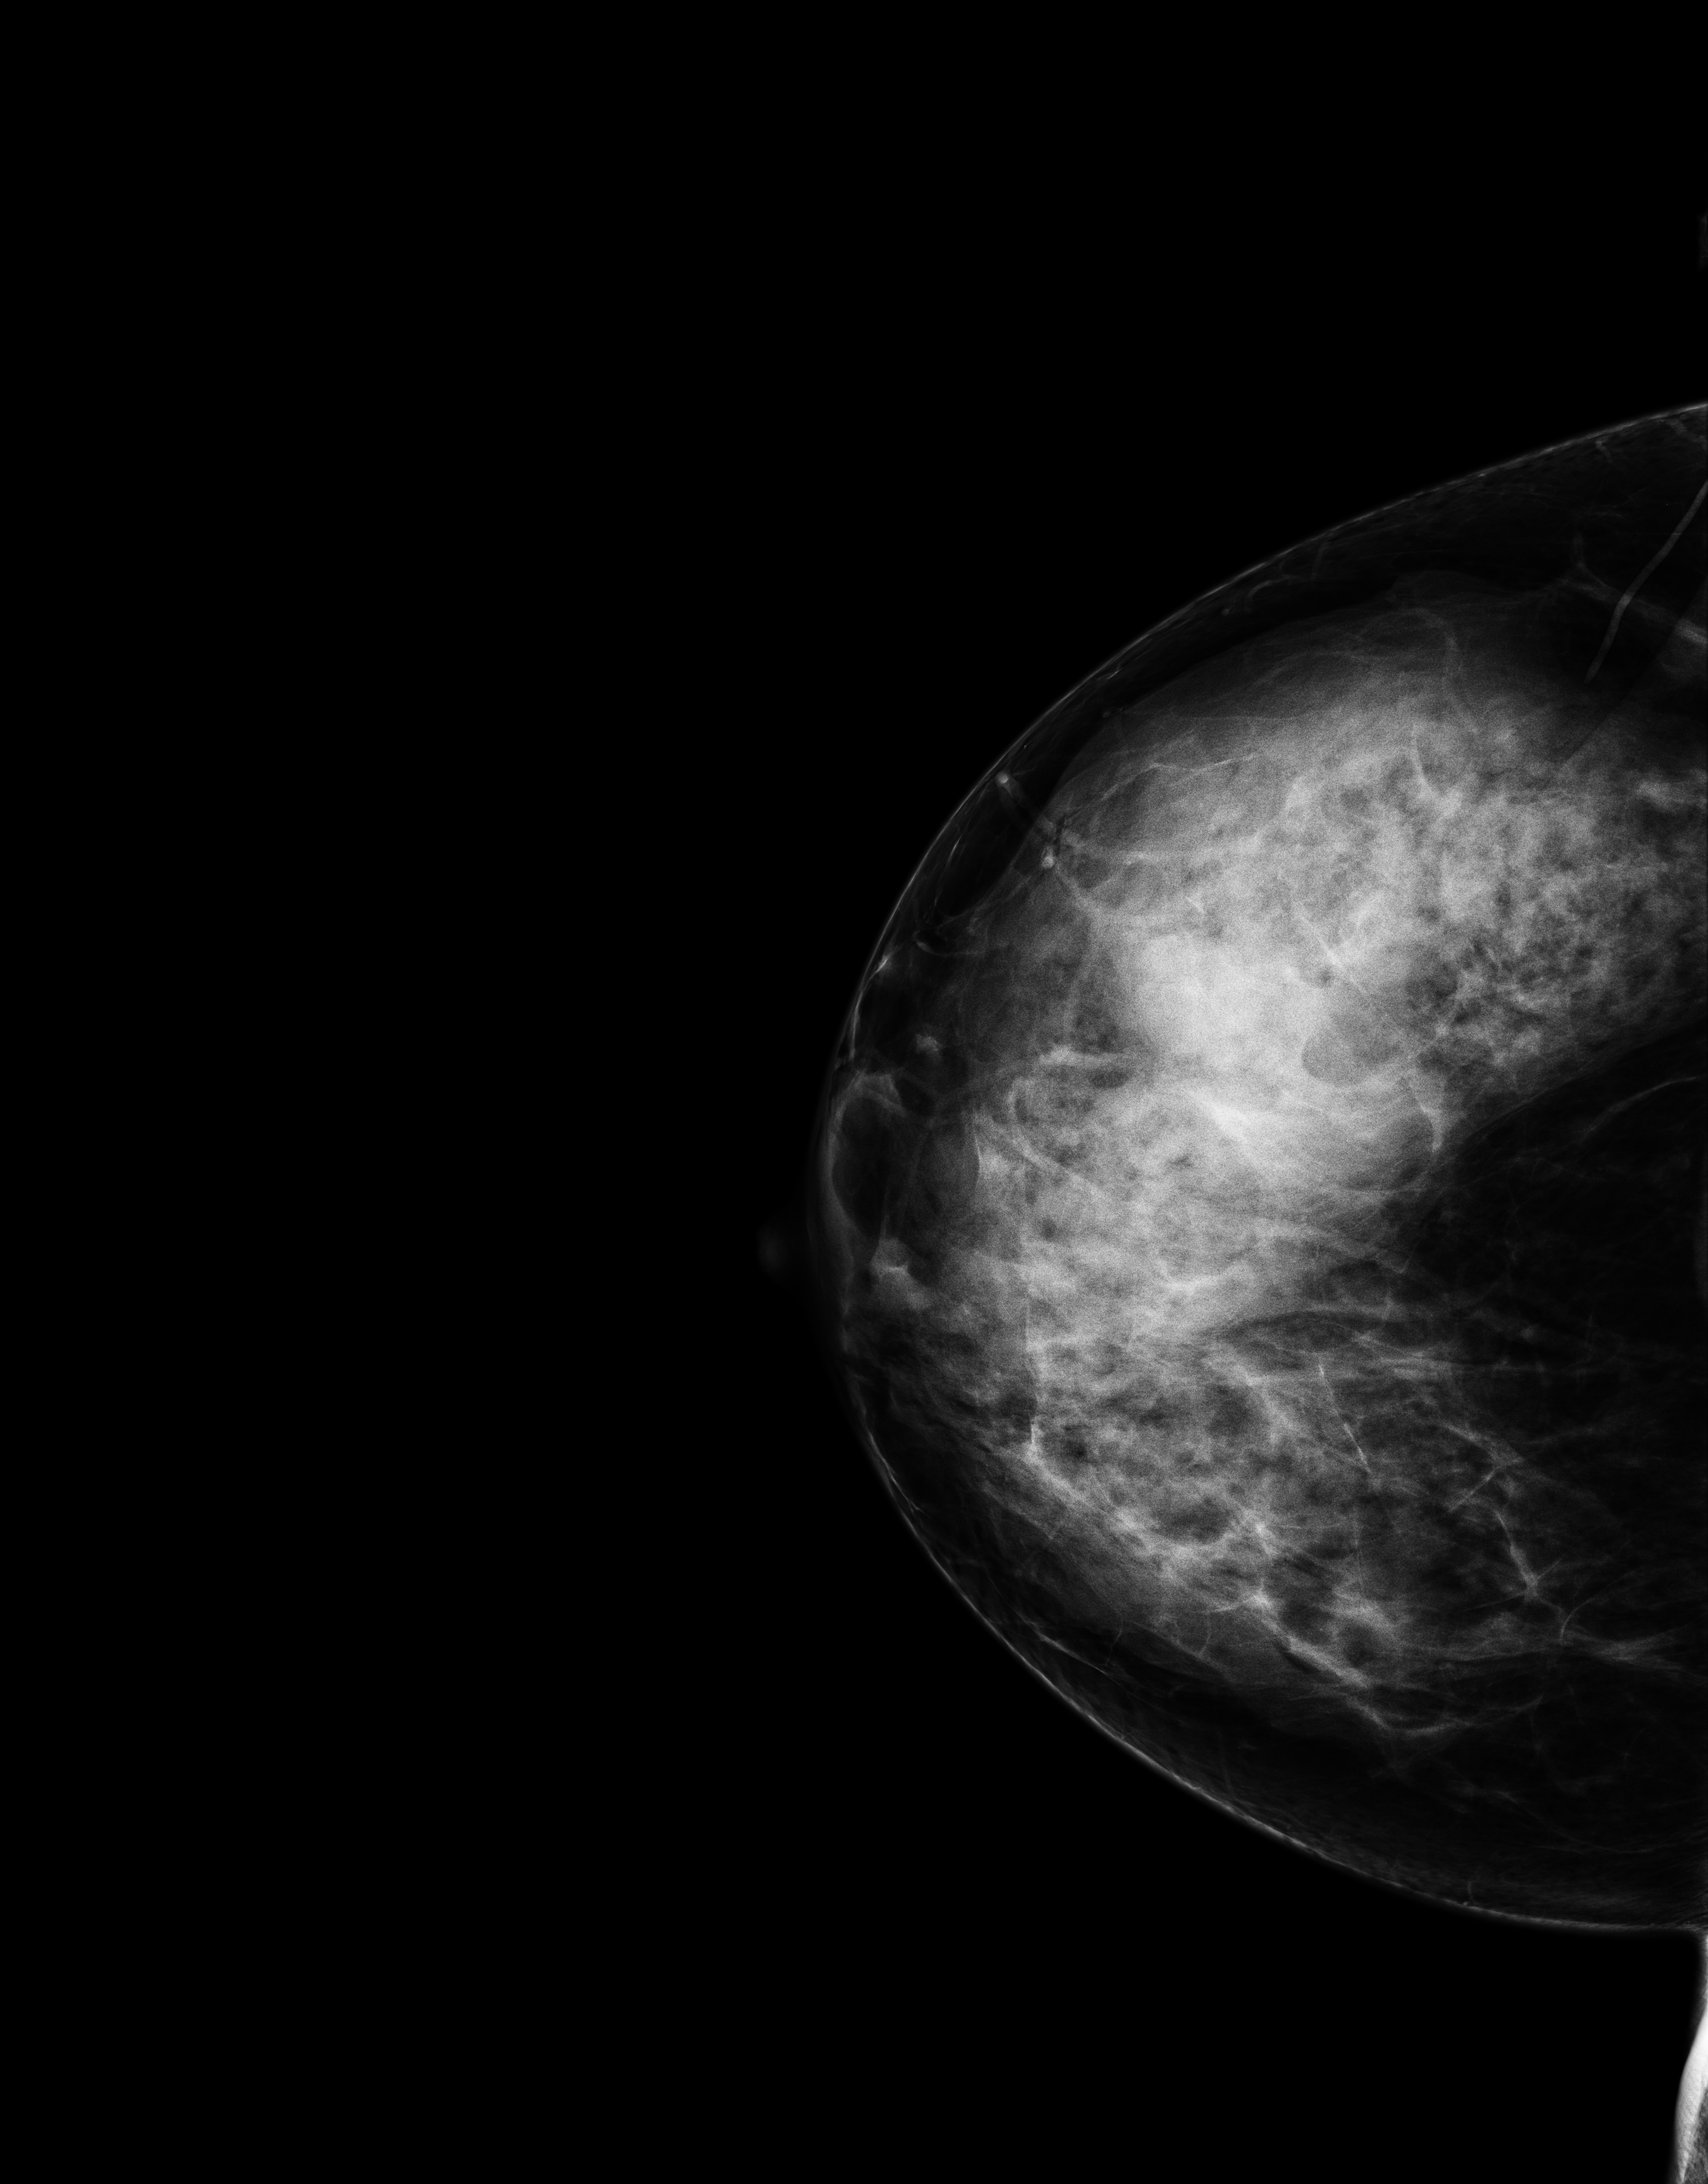
Digital mammogram (FFDM), right breast, cranio-caudal projection, screening examination, compressed breast thickness 62 mm. Patient: female, 43 years.
Breast density at the screening exam (both breasts): extremely dense (BI-RADS density category d). Final BI-RADS assessment for this screening round (tomosynthesis exam, both breasts): category 1. Recall: no recall after this screen.